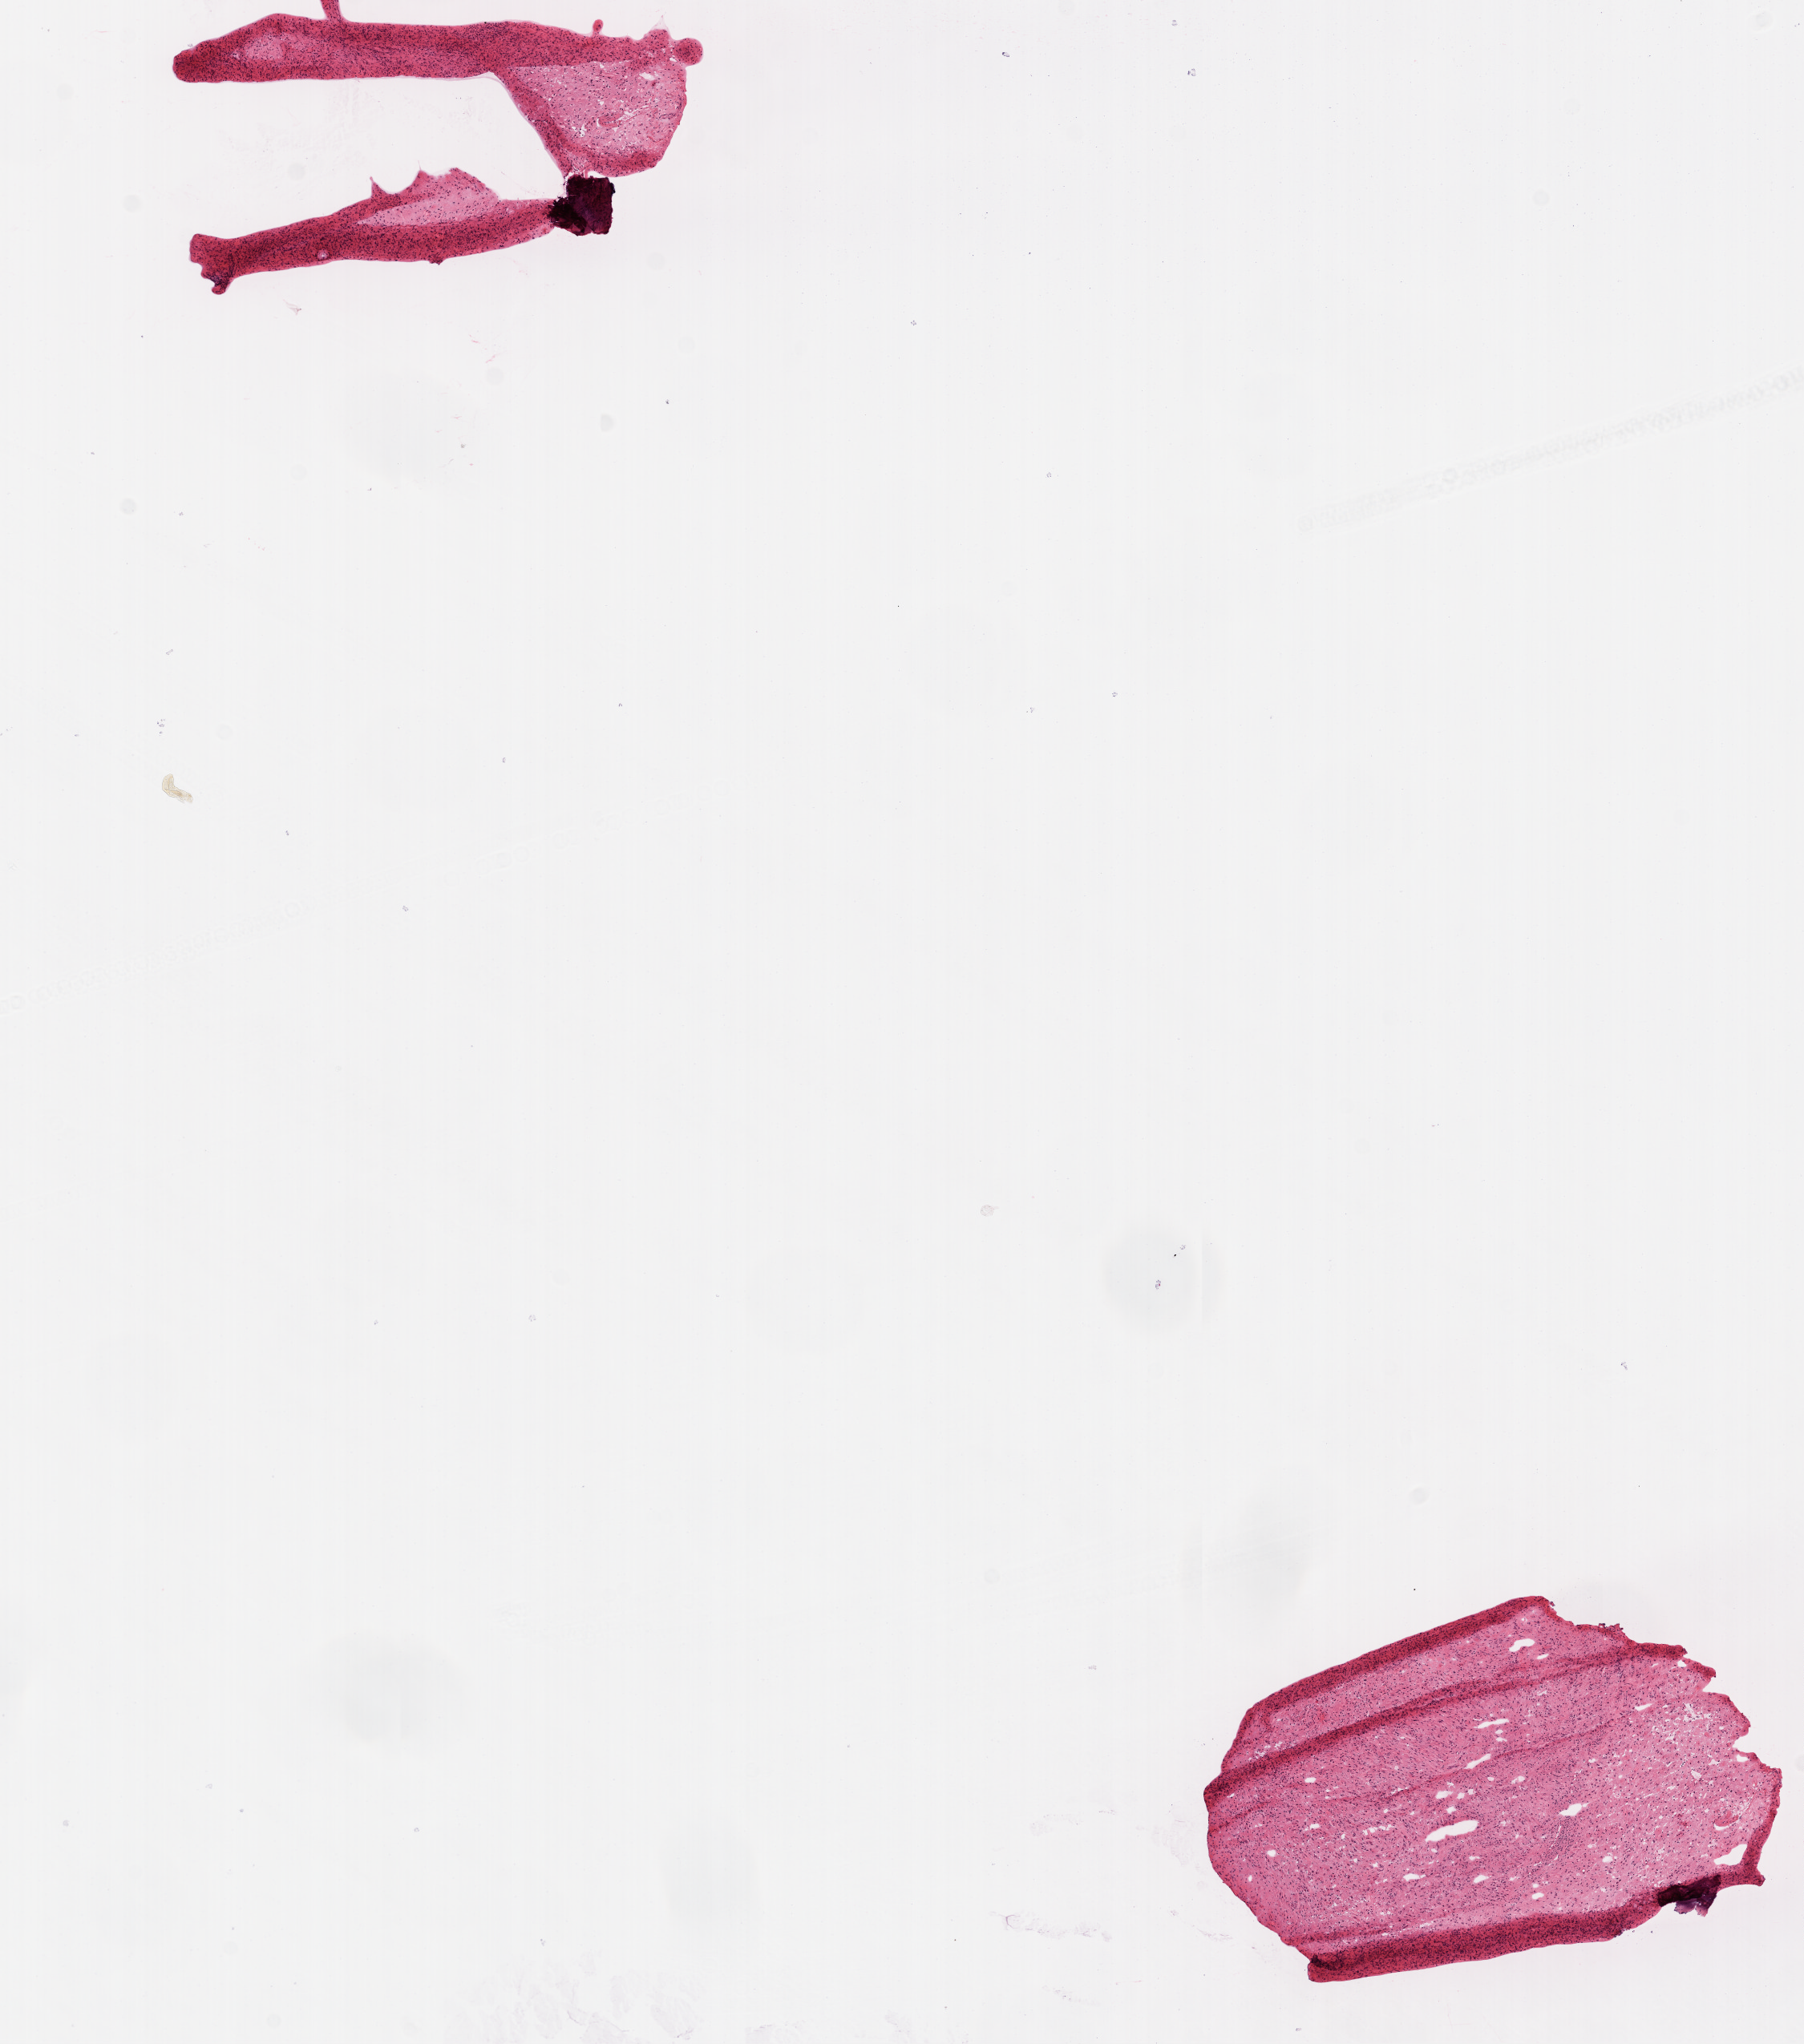
Digitized Hematoxylin and eosin (H&E) stained tissue section (whole slide), shown as a low-resolution overview of the whole scanned area (about 9.0 x 10.2 mm, from a 20x scan). Frozen section from the top of the tissue portion. Brain, primary tumour sample. Patient: male, age at initial diagnosis 36 years. Pathologist review of this section (percent, as recorded): tumour cells 90%, tumour nuclei 90%, normal cells 10%, stromal cells 0%, necrosis 0%.
Diagnosis: Glioblastoma.